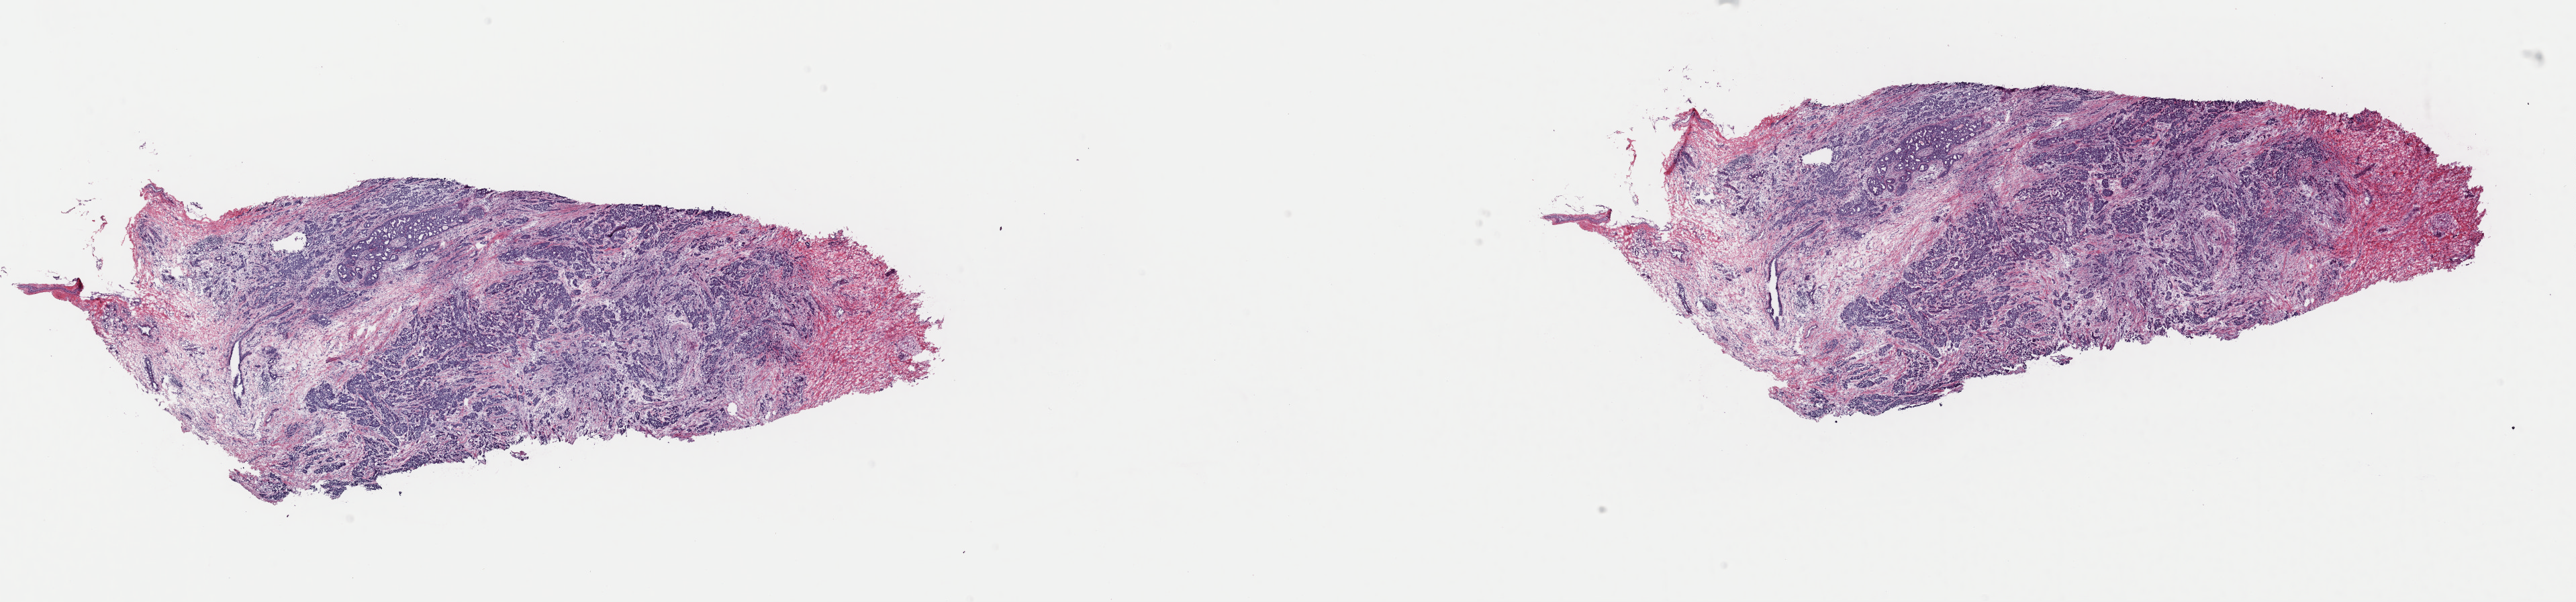
H&E whole-slide image — whole scanned area (about 30.3 x 7.1 mm, from a 40x scan) shown as a low-resolution overview. Frozen section from the top of the tissue portion. Sample: primary tumour, breast. Patient: female, age at initial diagnosis 46 years. Composition of this section per pathologist review: tumour cells 60%, tumour nuclei 80%, normal cells 0%, stromal cells 39%, necrosis 1%. Infiltration values recorded for this section: lymphocyte infiltration 2%, monocyte infiltration 0%, neutrophil infiltration 0%.
TNM: T2 N0 M0. Laterality: left. AJCC pathologic stage: IIA (7th edition). Diagnosis: Lobular carcinoma, NOS.